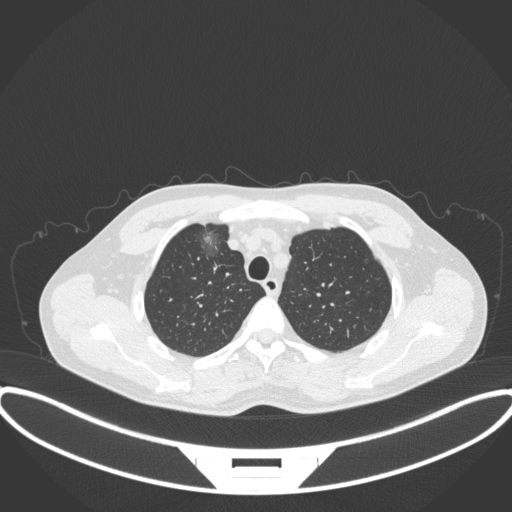
Chest CT, one axial slice. Slice 297 of 395 in the series (ordered by position). Reconstruction kernel B31f. 120 kVp. Lung window (W 1500 / L -600 HU). 1 mm slice thickness. 512 × 512 image matrix, field of view 424 × 424 mm. Patient: male, 60 years. Case-level facts recorded for this patient, not image findings: clinical TNM (as recorded): T1c N0 M0.
Structures marked on this image (bounding box drawn by a radiologist):
- lung tumour (recorded histology: adenocarcinoma): bounding box <197,226,231,261> (left, top, right, bottom; pixels)